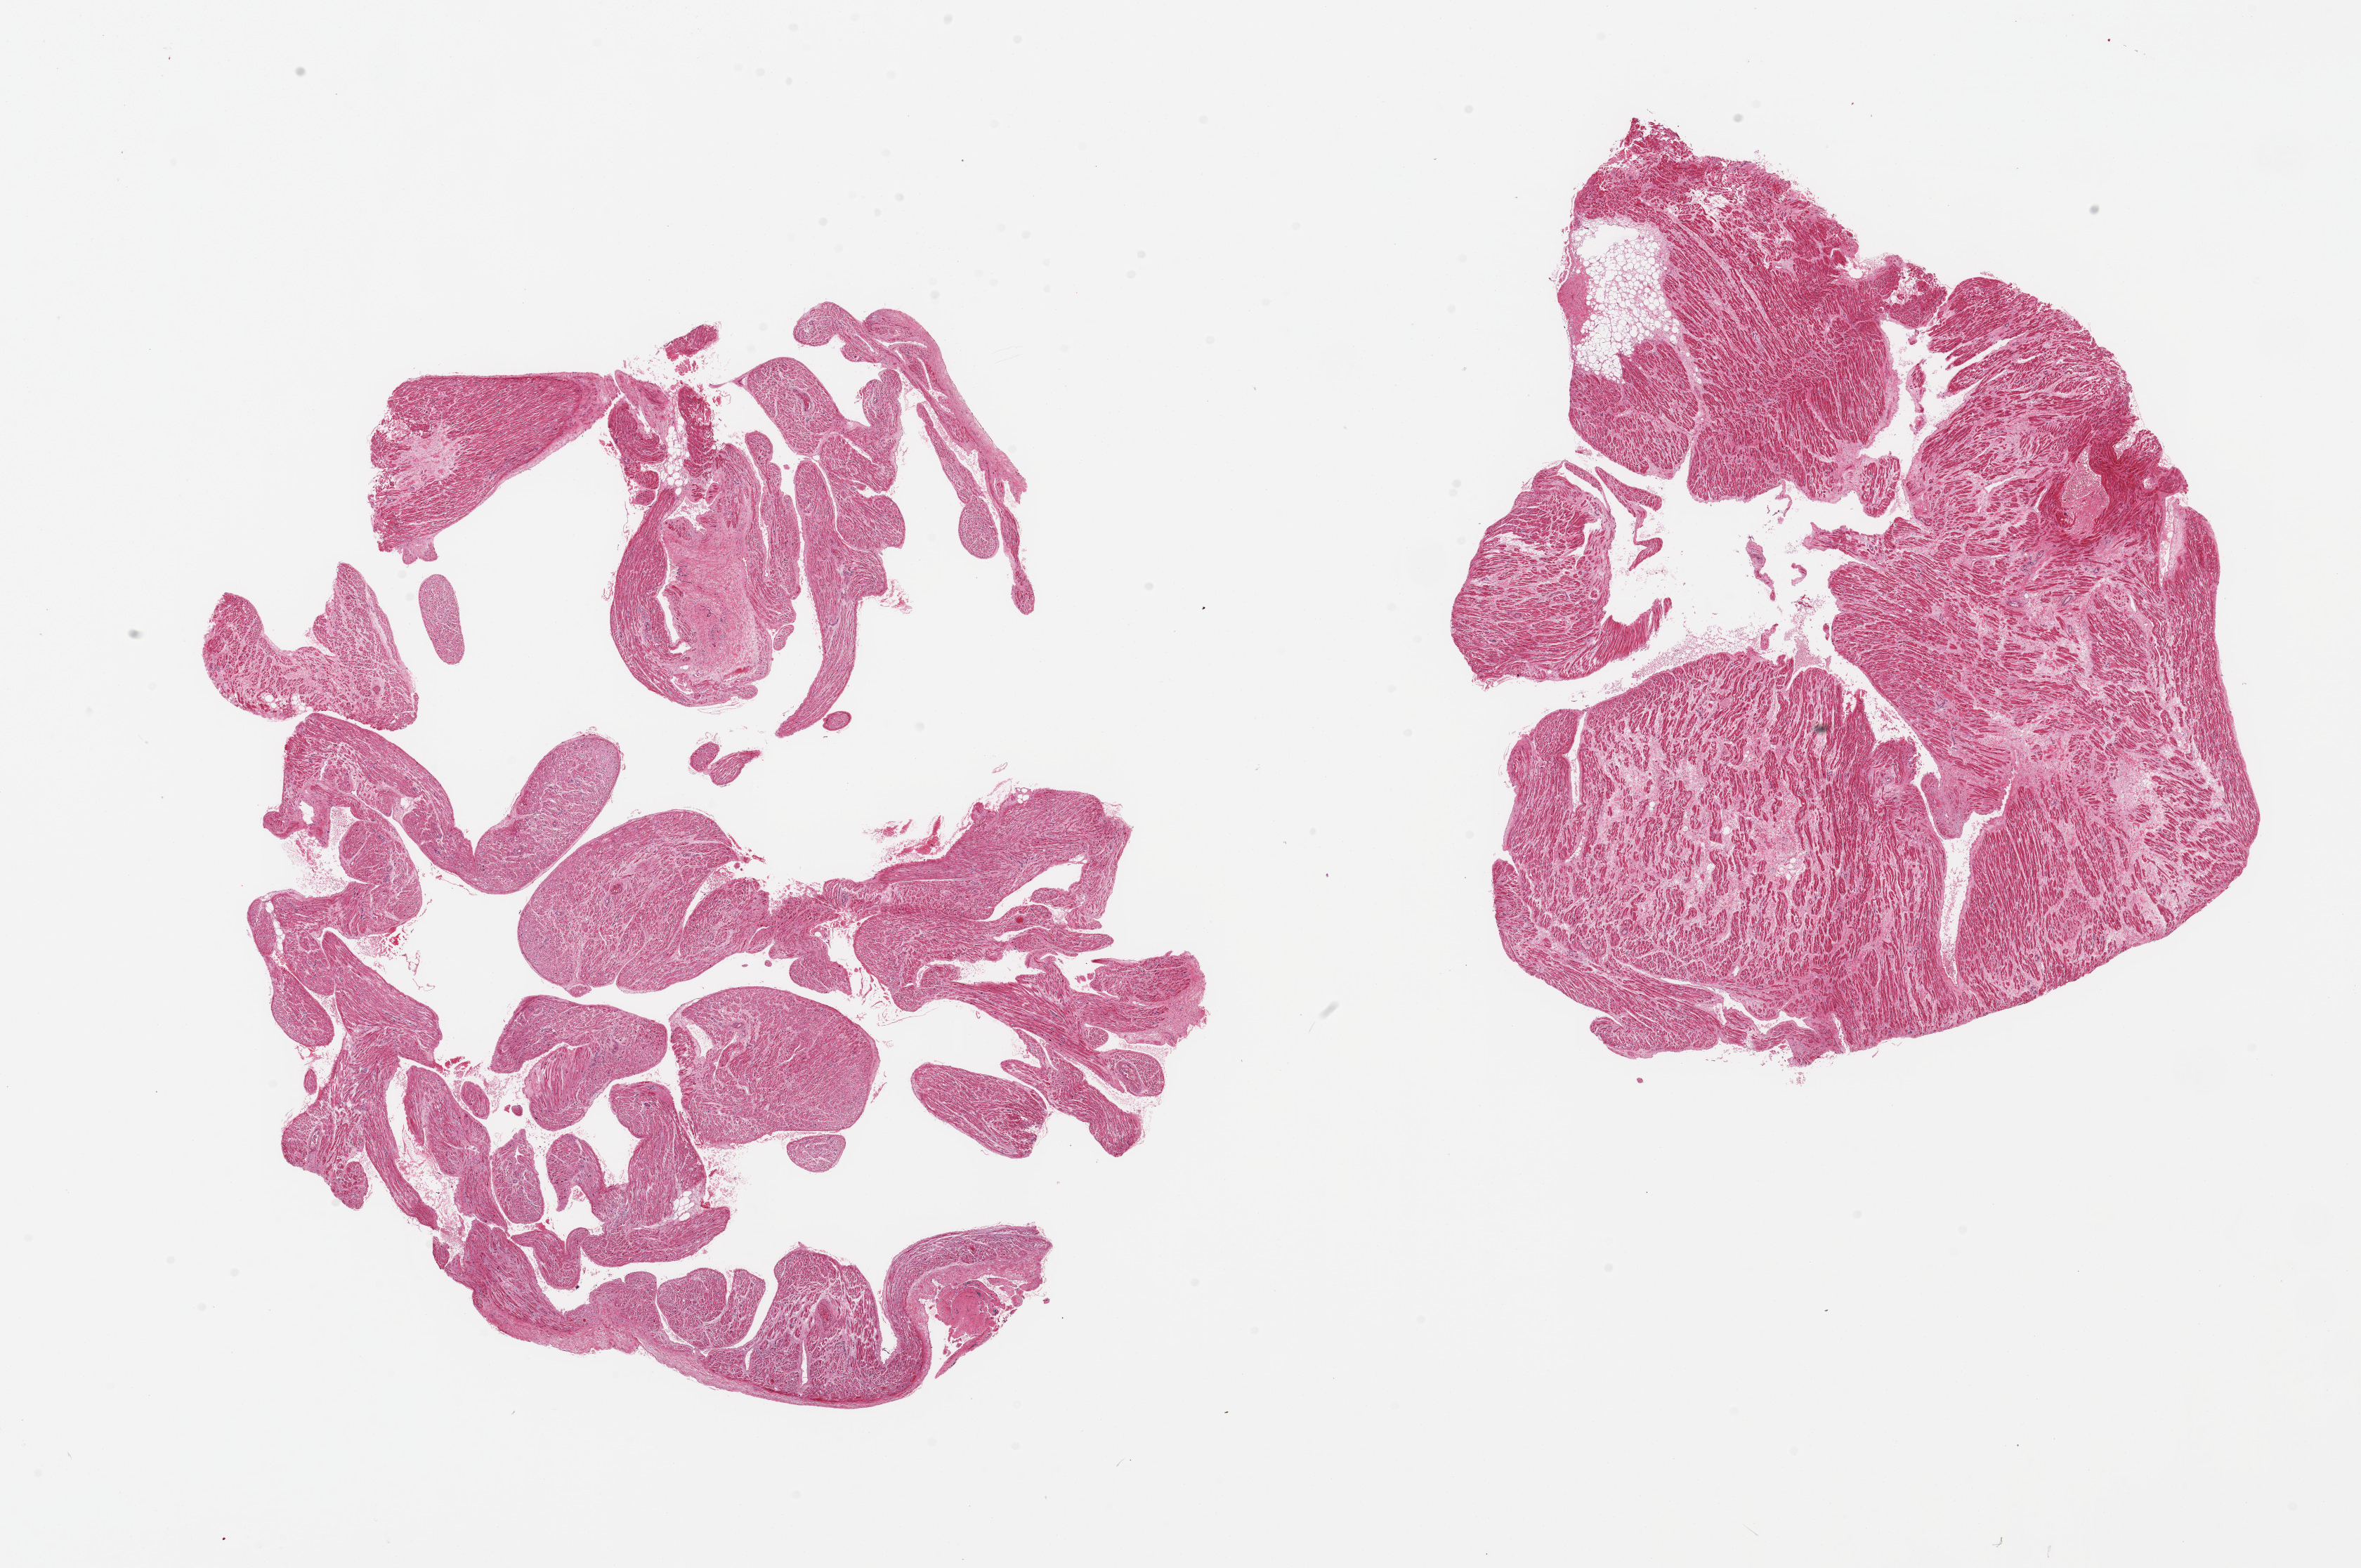
Haematoxylin and eosin whole-slide image — whole scanned area (about 26.6 x 17.7 mm, acquisition: 20x scan) shown as a low-resolution overview; PAXgene-fixed paraffin-embedded (PFPE) section; target tissue: auricular appendage; donor tissue sample. Male donor.
Pathologist's review note for this sample: 2 pieces, no abnormalities.